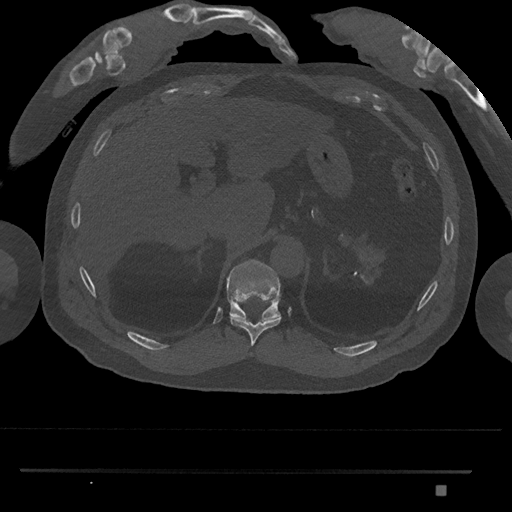
CT including the spine, one axial slice; position 977 of 1134 along the scan axis; reconstruction kernel Br40s/3; 120 kVp; bone window (W 1800 / L 400 HU); 0.5 mm slice thickness; 512 × 512 image matrix, field of view 429 × 429 mm. Male patient, age 65 years. Case-level facts recorded for this patient, not image findings: primary cancer: prostate.
Outlined on this slice (semi-automatically segmented with operator editing):
- T10 vertebra: bounding box [x1, y1, x2, y2] px = [230, 317, 281, 346]
- T11 vertebra: [226, 259, 281, 319]